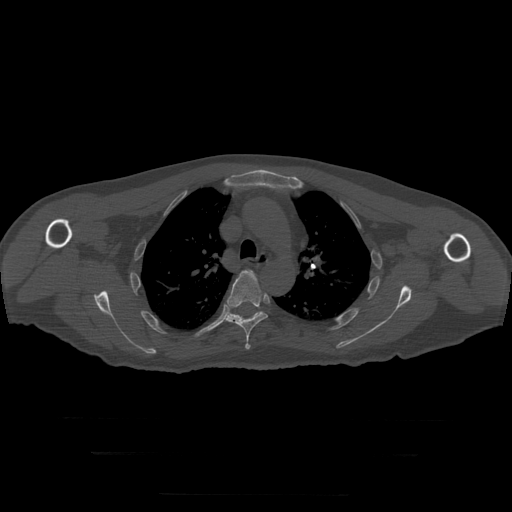
CT including the spine, one axial slice. Slice 223 of 397 in the series (ordered by position). Reconstruction kernel STANDARD. Bone window (W 1800 / L 400 HU). 1.25 mm slice thickness. 512 × 512 image matrix. Patient age 73 years. Case-level facts recorded for this patient, not image findings: primary cancer: prostate.
Annotated regions visible in this slice (semi-automatically segmented with operator editing):
- T4 vertebra: bounding box [x1, y1, x2, y2] px = [245, 271, 249, 273]
- T5 vertebra: [225, 271, 268, 350]
- T6 vertebra: [229, 312, 261, 320]